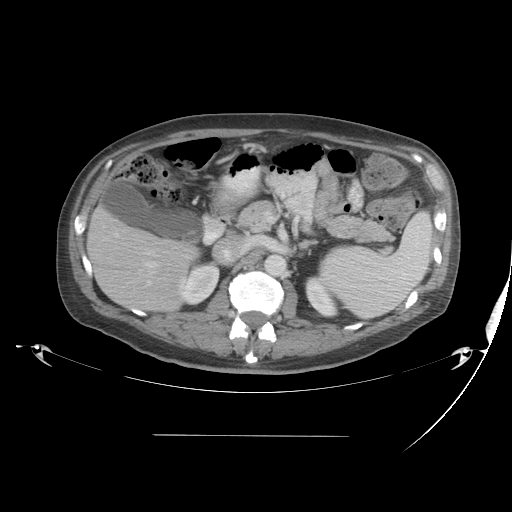
Contrast-enhanced abdominal CT, one axial slice; reconstruction kernel STANDARD; 120 kVp; soft-tissue window (W 400 / L 40 HU); 5 mm slice thickness; 512 × 512 image matrix, field of view 486 × 486 mm. Male patient, age 65 years. Case-level facts recorded for this patient, not image findings: diagnosis: colorectal cancer liver metastases, imaged before liver resection; multiple liver metastases: yes; largest metastasis: 11 cm; disease in both lobes: yes.
Structures marked on this image (manually delineated by an expert):
- hepatic veins: box from (x=146, y=263) to (x=157, y=267) px
- liver: (x=89, y=209)–(x=196, y=312)
- portal vein (with intrahepatic branches): (x=102, y=230)–(x=155, y=286)